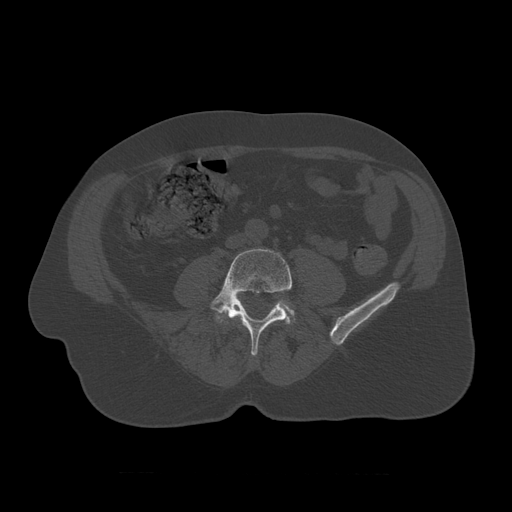
CT including the spine, one axial slice. Slice 276 of 450 in the series (ordered by position). Bone window (W 1800 / L 400 HU). 512 × 512 image matrix, field of view 405 × 405 mm. Patient age 75 years. Case-level facts recorded for this patient, not image findings: primary cancer: prostate.
Structures marked on this image (semi-automatically segmented with operator editing):
- L4 vertebra: bounding box [x1, y1, x2, y2] px = [210, 249, 293, 357]
- L5 vertebra: [217, 299, 296, 323]